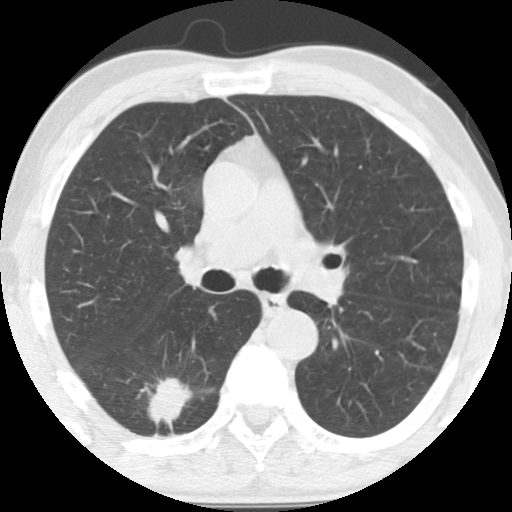
Axial slice from a low-dose chest CT screening exam, baseline screening round, lung window (W 1500 / L -600 HU), 2.5 mm slice thickness, standard (soft-tissue) reconstruction kernel (STANDARD), slice 49 of 135 in the series. Male participant, aged 64 years at enrolment. Current smoker at enrolment.
Lesion marked by an expert reader, bounding box (x1, y1, x2, y2) in pixels: (118, 366, 192, 433). Reader record for this screening exam (exam-level; its link to the box is not recorded): non-calcified nodule or mass ≥4 mm, right lower lobe, 36 × 26 mm, spiculated (stellate) margins, soft tissue attenuation. Official screen result: positive, change unspecified: nodule(s) >= 4 mm or enlarging nodule(s), mass(es), or other non-specific abnormalities suspicious for lung cancer. Lung cancer was diagnosed 20 days after this screen: adenocarcinoma, NOS, right lower lobe, moderately differentiated (G2), stage IA (AJCC 6th edition), 28 mm at pathology.